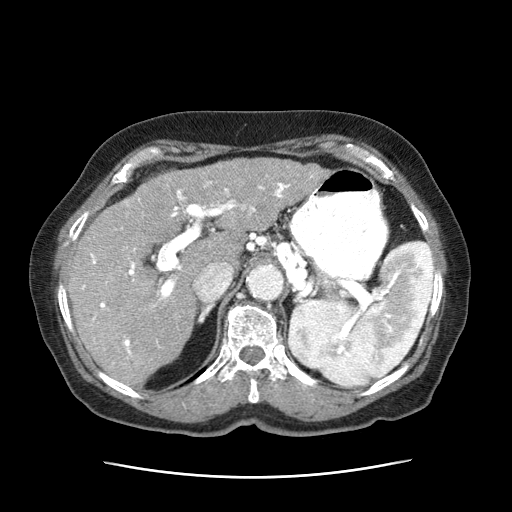
Contrast-enhanced abdominal CT (liver protocol), one axial slice. Slice 42 of 63 in the series (ordered by position). Reconstruction kernel STANDARD. 120 kVp. Intravenous contrast given. Soft-tissue window (W 400 / L 40 HU). 2.5 mm slice thickness. 512 × 512 image matrix, field of view 360 × 360 mm. Patient: female, 79 years. Case-level facts recorded for this patient, not image findings: diagnosis: hepatocellular carcinoma (patient treated with transarterial chemoembolisation; whether this scan precedes or follows treatment is not stated here); TNM stage (as recorded): Stage-II; Child-Pugh class: B; tumour nodularity: multinodular; tumour size: 5 cm.
Structures marked on this image (semi-automatic segmentation, software-assisted and operator-edited):
- abdominal aorta: bounding box (x1, y1, x2, y2) in pixels: (247, 266, 283, 301)
- liver parenchyma outside the tumour (the mass and vessels are separate outlines, so this box may not span the whole liver): (64, 176, 248, 389)
- mass: (168, 160, 330, 228)
- liver vessels: (80, 183, 290, 359)